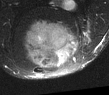
MRI of an extremity soft-tissue mass, one axial slice; slice 34 of 52 in the series (ordered by position); T2-weighted fat-saturated; MR volume resampled by the dataset authors to the PET/CT grid (not the native acquisition matrix); 109 × 95 image matrix, field of view 106 × 93 mm. Male patient. From the clinical record (not read from this slice): histological type: synovial sarcoma; site of the primary tumour: left poplietal fossa.
Outlined on this slice (expert contour drawn on MRI and transferred to this co-registered scan by the dataset authors):
- gross tumour volume (mass): bounding box (x1, y1, x2, y2) in pixels: (24, 19, 73, 68)